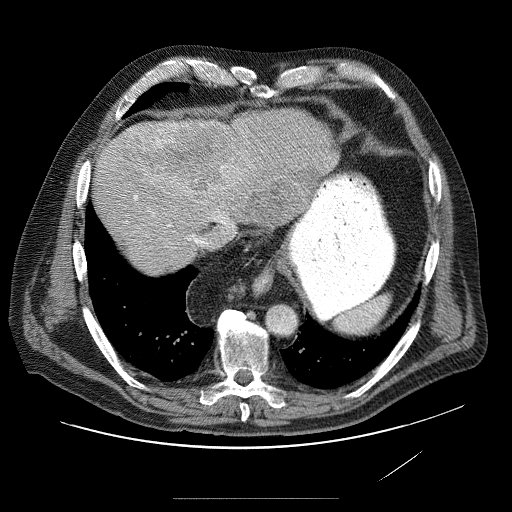
Contrast-enhanced abdominal CT (liver protocol), one axial slice. Position 70 of 89 along the scan axis. 120 kVp. Soft-tissue window (W 400 / L 40 HU). 512 × 512 image matrix, field of view 420 × 420 mm. From the clinical record (not read from this slice): diagnosis: hepatocellular carcinoma (patient treated with transarterial chemoembolisation; whether this scan precedes or follows treatment is not stated here); TNM stage (as recorded): Stage-IVA; Child-Pugh class: A.
Outlined on this slice (semi-automatically segmented with operator editing):
- liver parenchyma outside the tumour (the mass and vessels are separate outlines, so this box may not span the whole liver): box from (x=94, y=112) to (x=336, y=252) px
- mass: (x=122, y=118)–(x=307, y=224)
- liver vessels: (x=111, y=123)–(x=261, y=237)